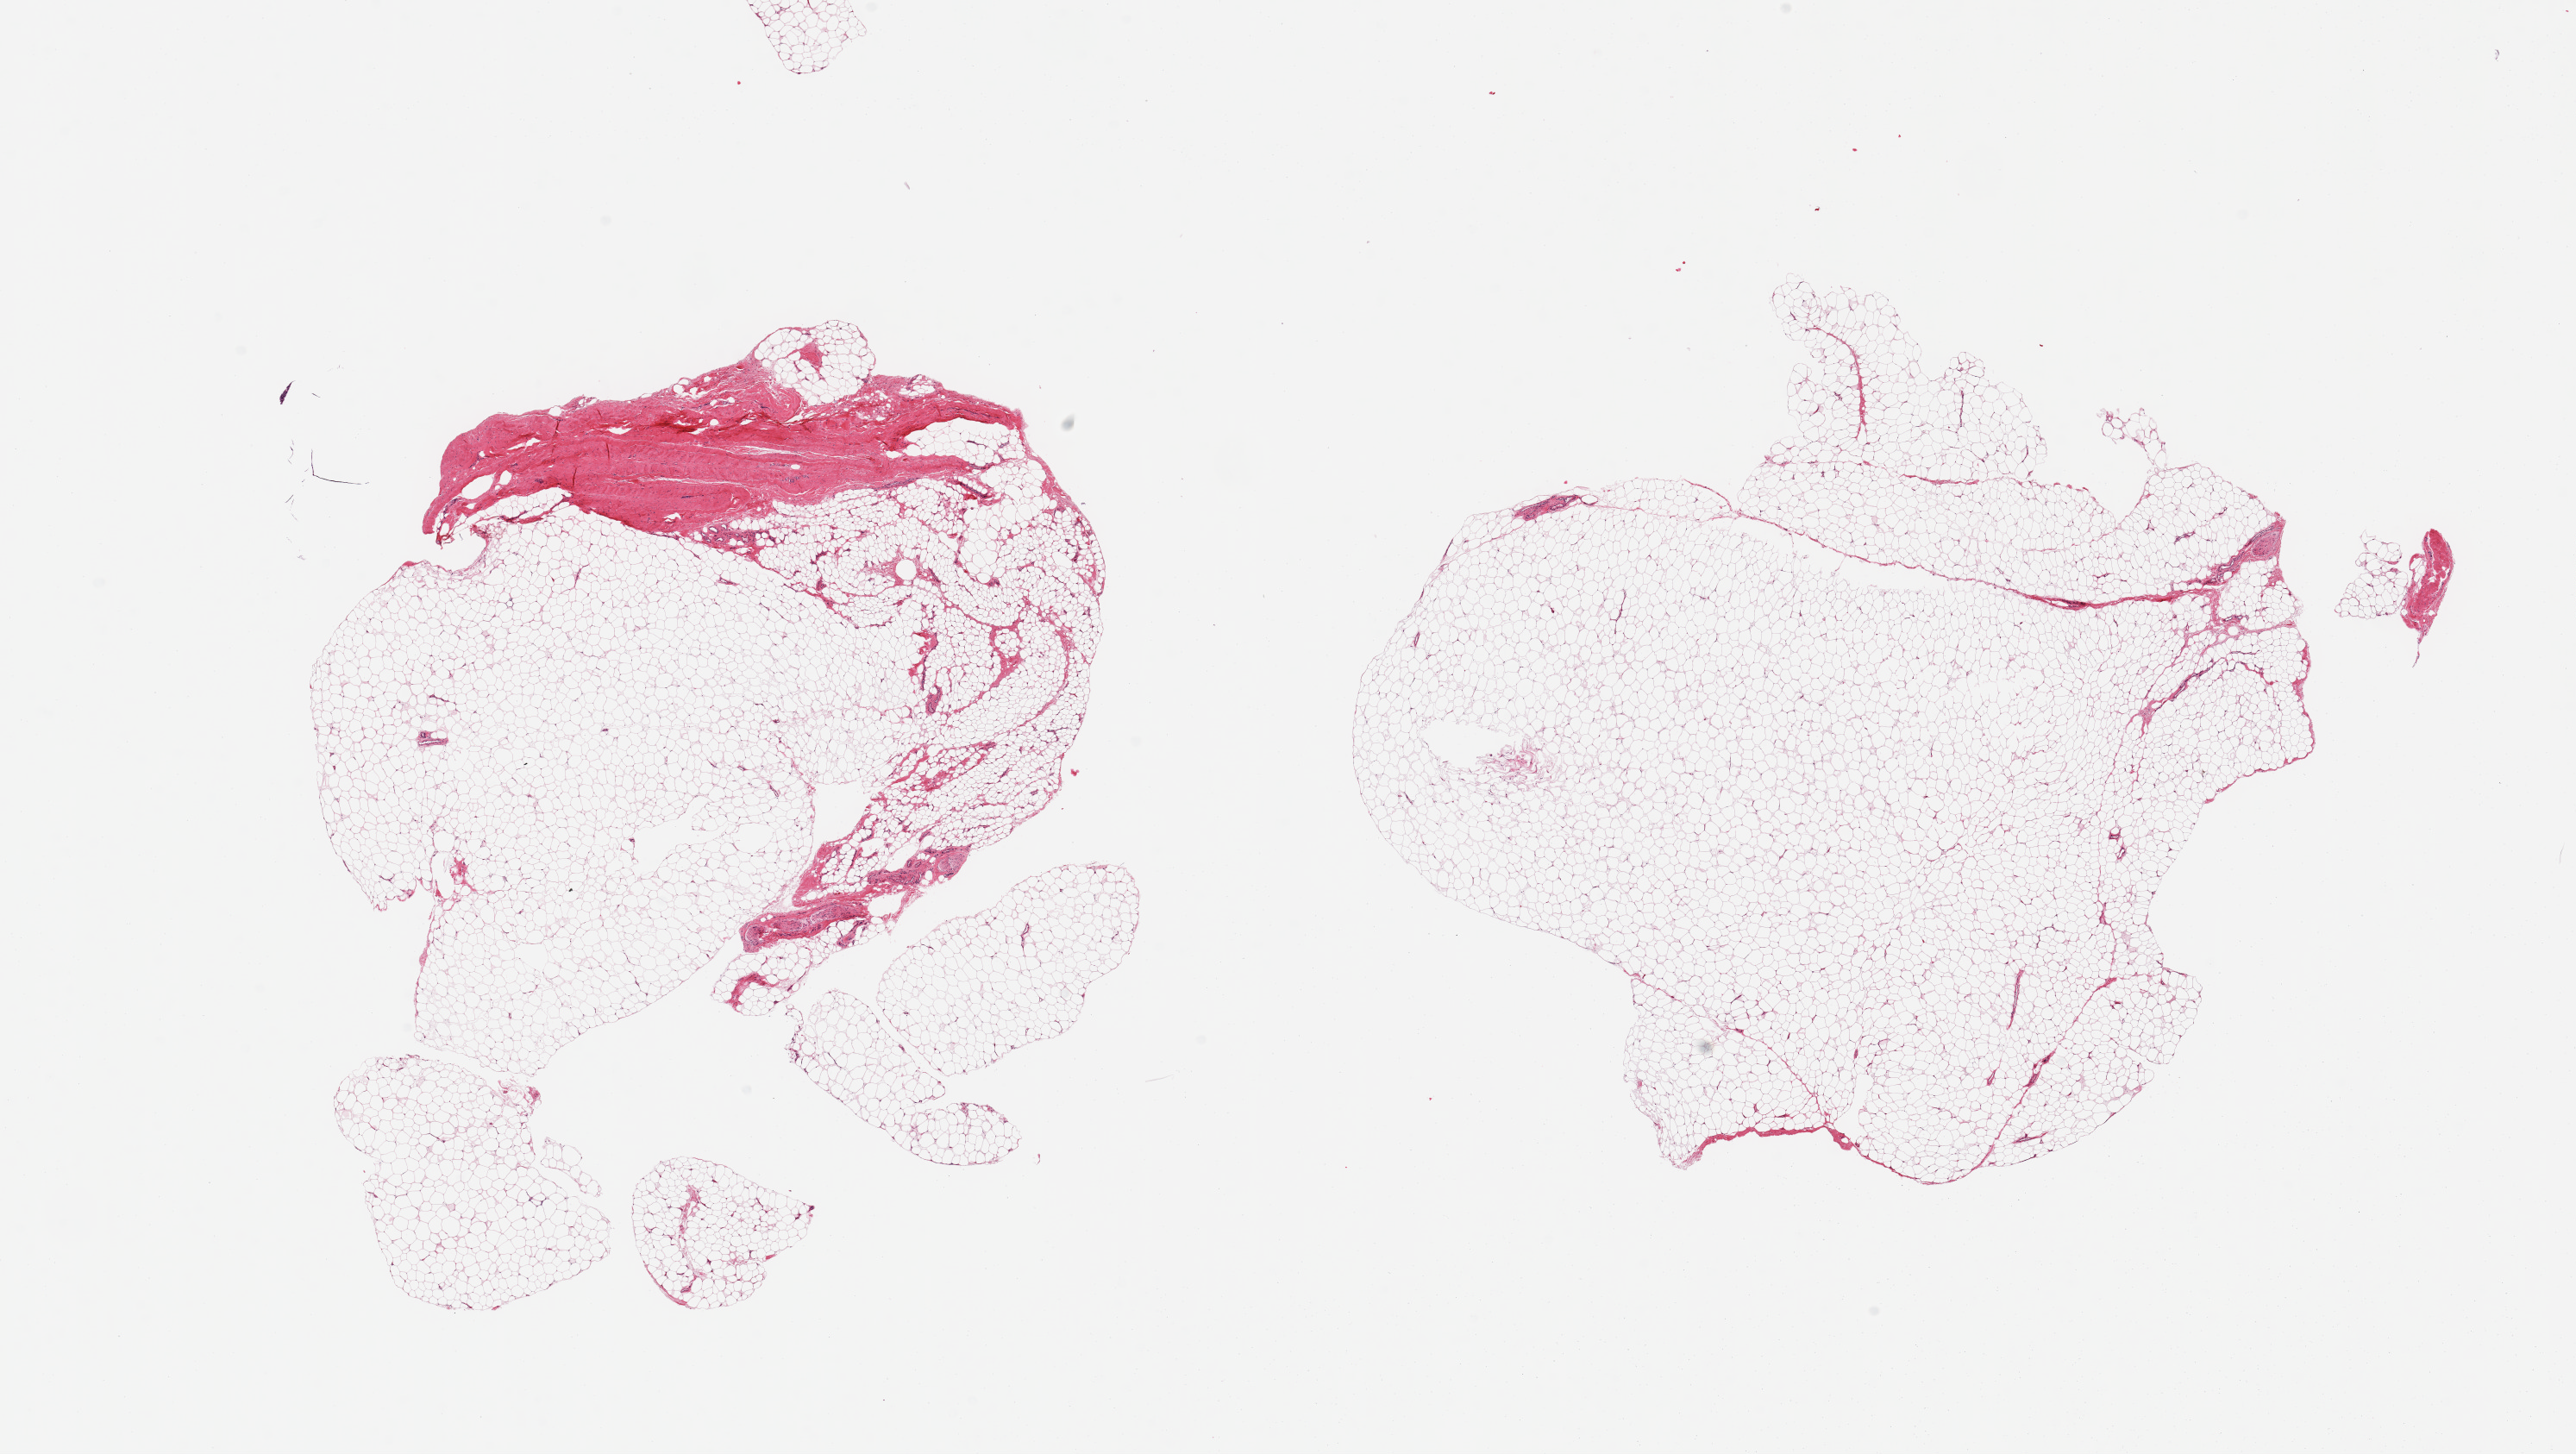
Haematoxylin and eosin whole-slide image, brightfield, whole scanned area (about 23.6 x 13.3 mm, slide scanned at 20x) shown as a low-resolution overview, PAXgene-fixed, paraffin-embedded tissue, sampled site (target tissue): adipose tissue, tissue donor sample. Donor sex: male.
* pathologist's review note for this sample: 2 pieces, ~10% fascia/tendon